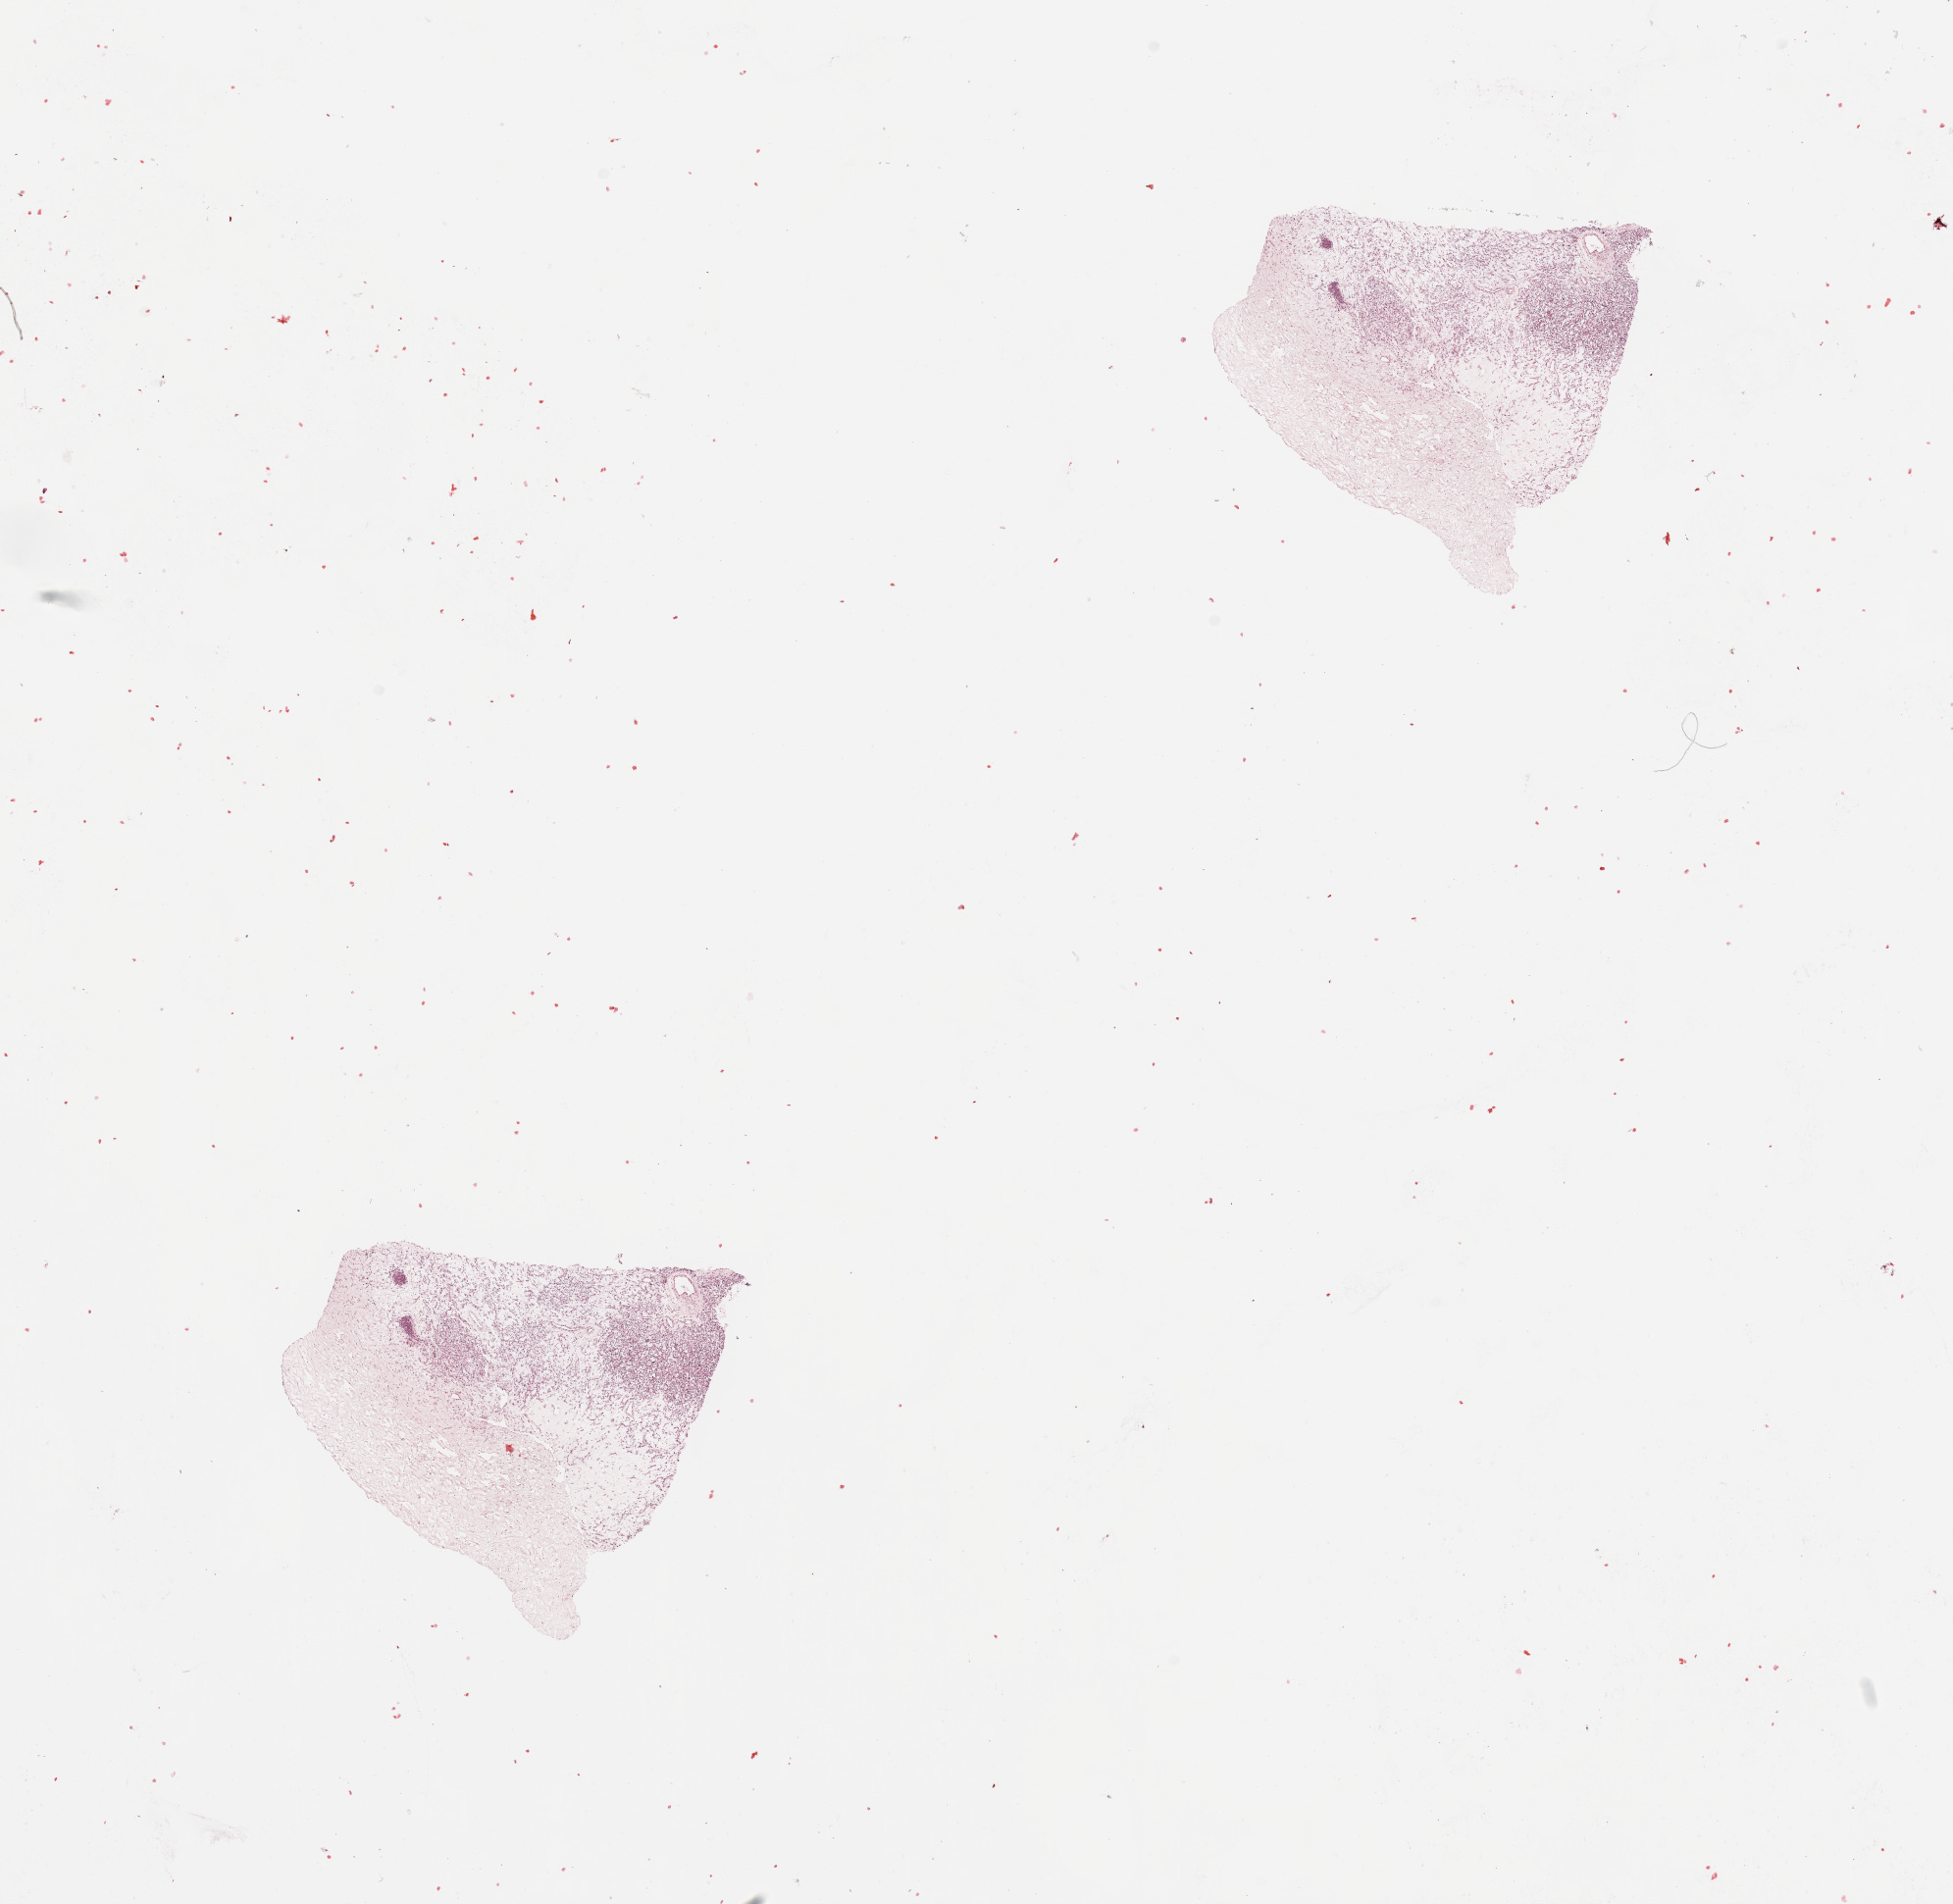
Digitized H&E tissue section (whole slide) — whole scanned area (about 15.8 x 15.4 mm, acquisition: 20x scan) shown as a low-resolution overview. Tumour tissue sample, sampled site: kidney. Female, 64 y/o. Histologic grade: G2 (moderately differentiated). Pathologist review of this section (percent, as recorded): tumour nuclei 80%, necrosis 0%.
- AJCC pathologic stage: III
- diagnosis: Renal cell carcinoma, NOS